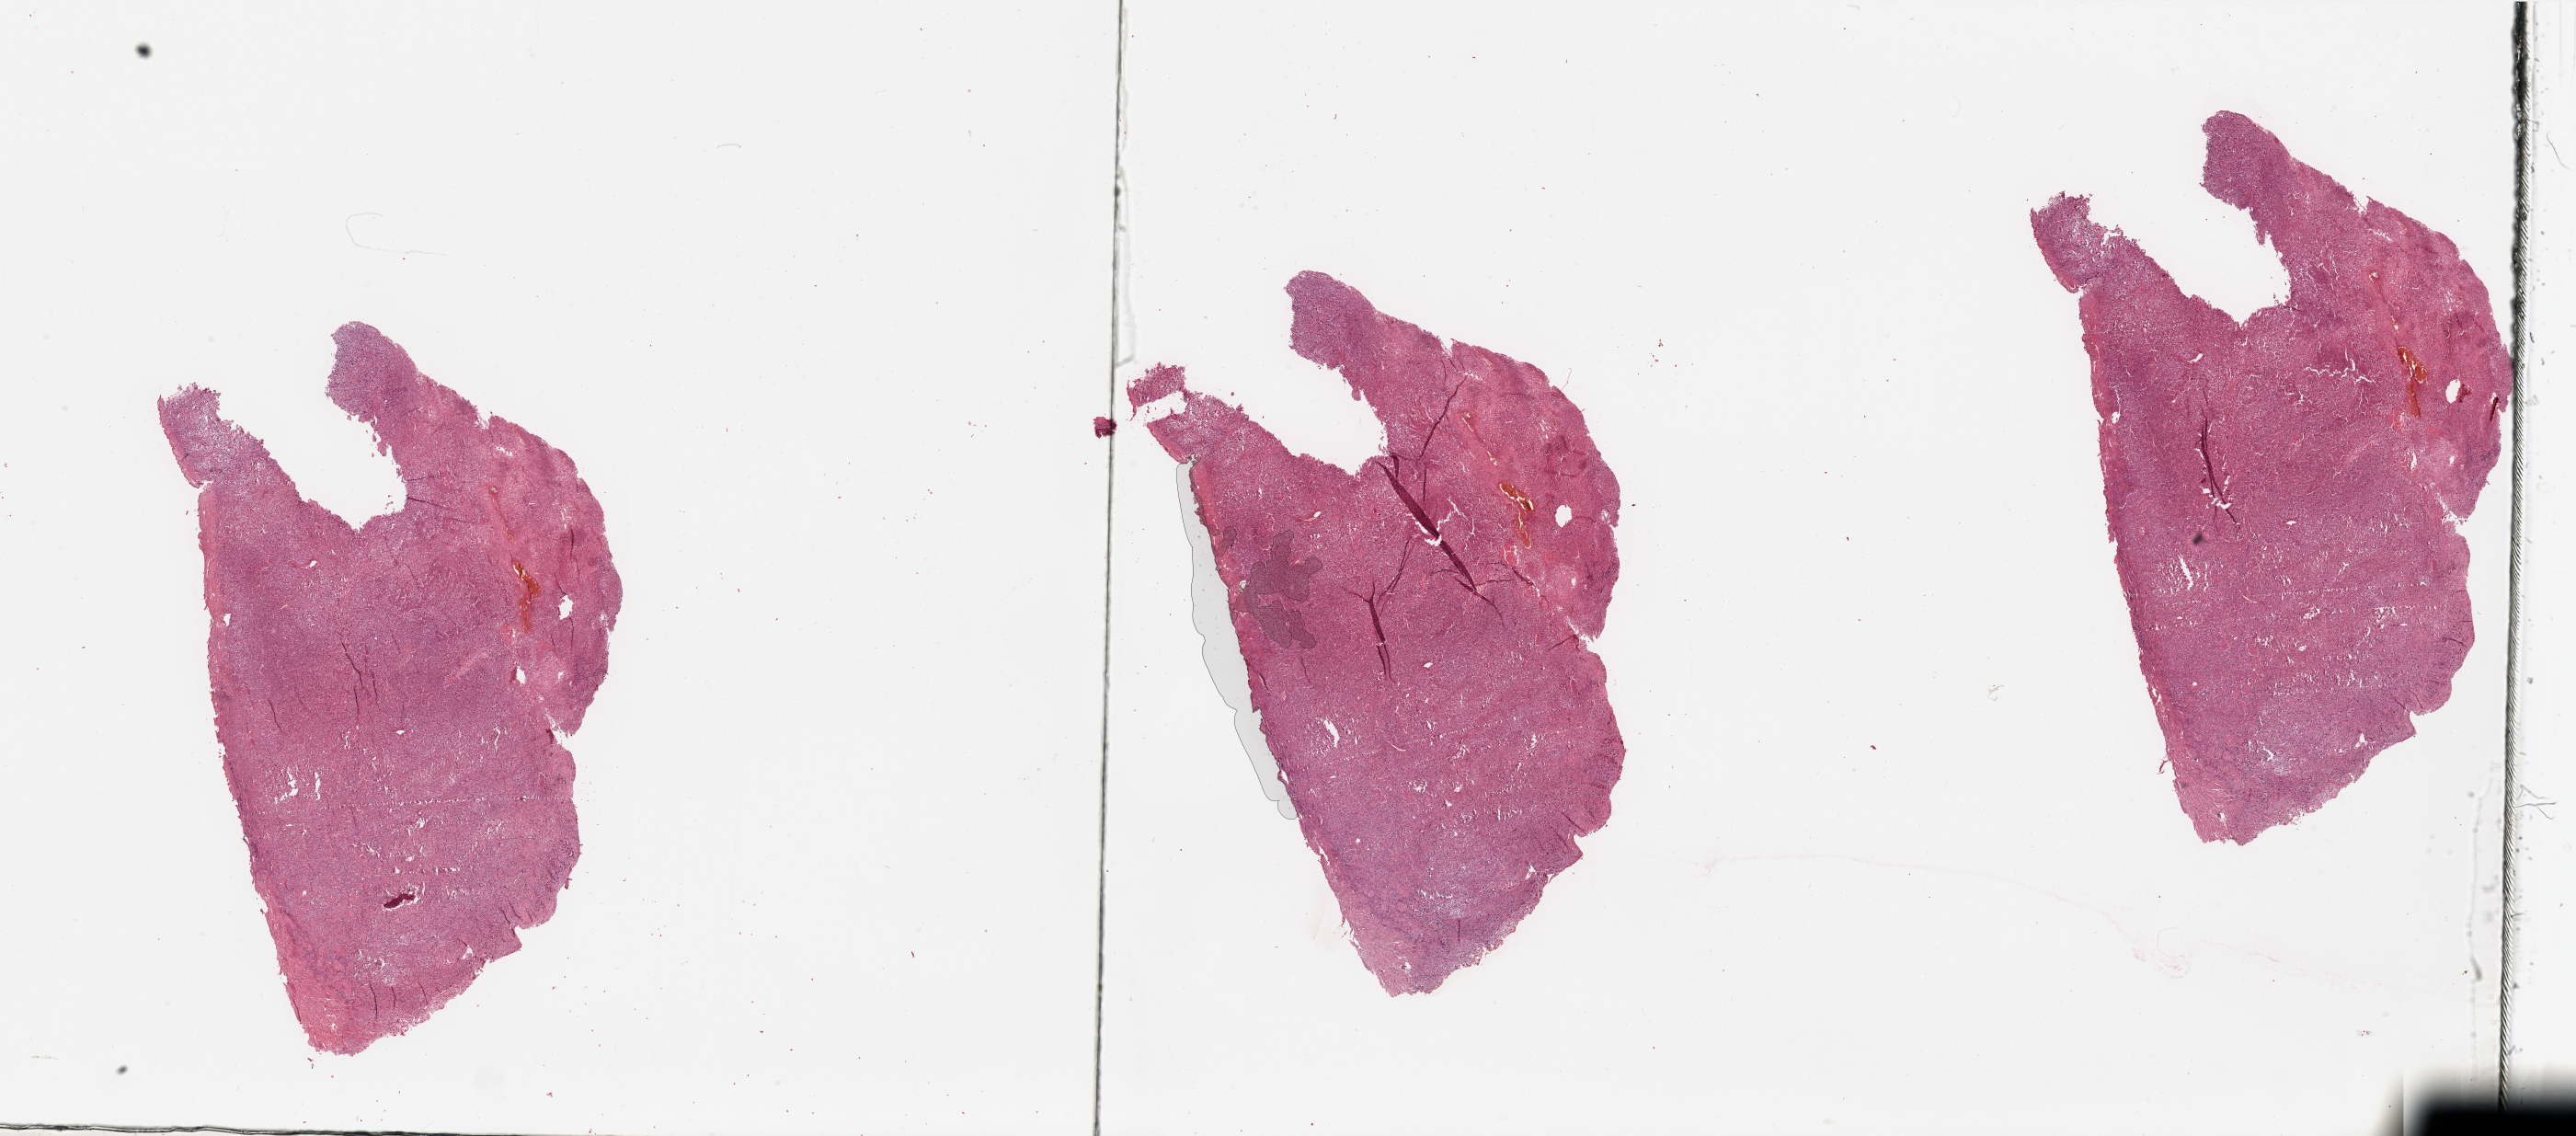
H&E-stained whole-slide image — low-resolution overview of the scanned area, about 44.3 x 19.5 mm (from a 20x scan). 80-year-old female patient.
Primary tumour site (as recorded): gynecologic. Patient diagnosis (cohort enrolment): sarcoma (site not recorded at cohort level).